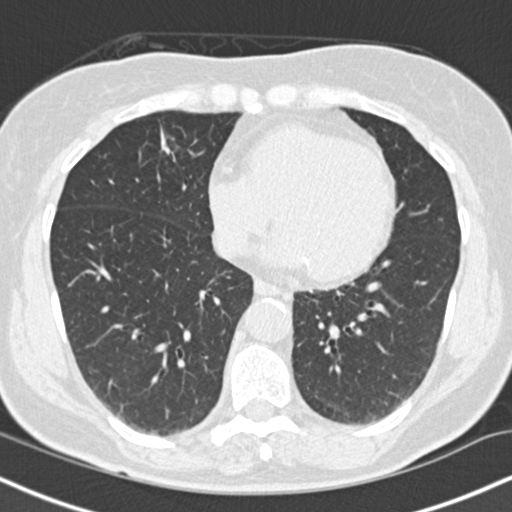
Axial slice from a low-dose chest CT screening exam. First (baseline) screen. Lung window (W 1500 / L -600 HU). Standard (soft-tissue) reconstruction kernel (B30f). Slice 90 of 145 in the series. Female, age 66 years at enrolment. Current smoker at enrolment.
• Expert reader's lesion annotation, bounding box (x1, y1, x2, y2) in pixels: (141, 122, 189, 169).
• The exam's reader record, not a measurement of the box and not confirmed to be the same lesion: non-calcified nodule or mass ≥4 mm, right lower lobe, 10 × 8 mm, smooth margins, soft tissue attenuation.
• Participant outcome: lung cancer diagnosed 96 days after this screen — squamous cell carcinoma, keratinizing, NOS, right upper lobe, right middle lobe, poorly differentiated (G3), stage IA (AJCC 6th edition), 14 mm at pathology.